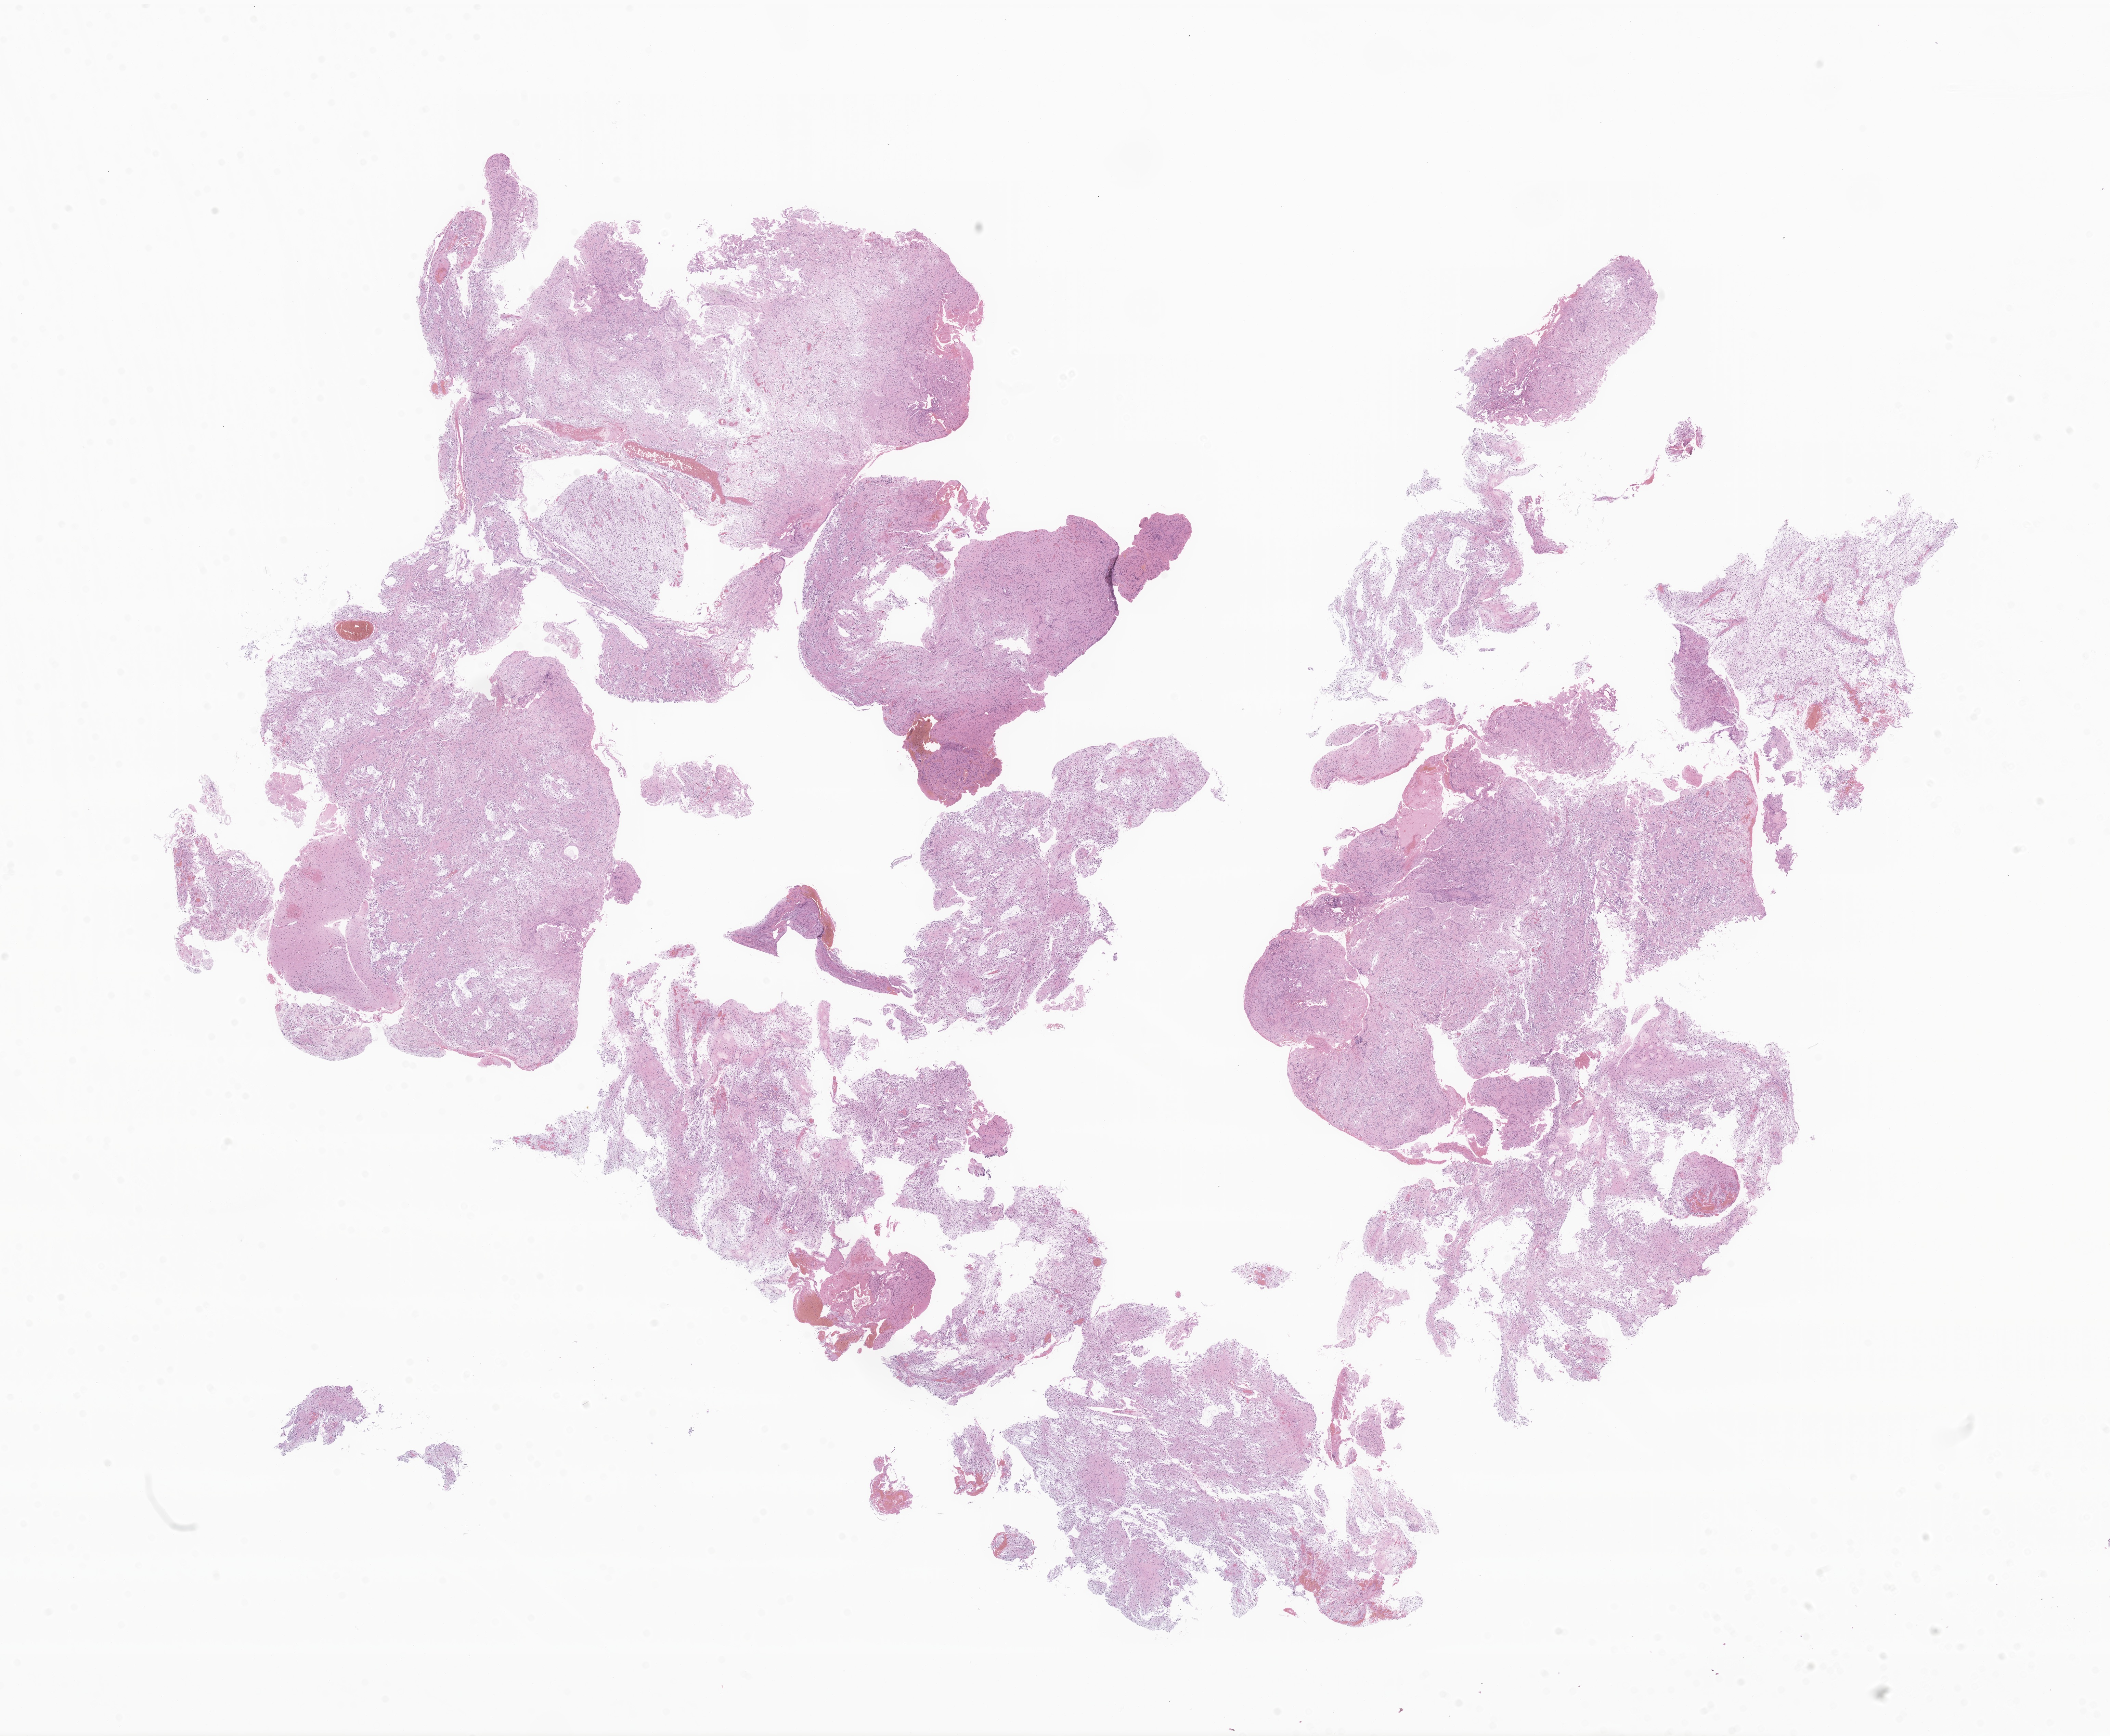
Whole-slide image, haematoxylin and eosin stain of tumor tissue from the brain — whole scanned area (about 26.0 x 21.4 mm) shown as a low-resolution overview, formalin-fixed, paraffin-embedded (FFPE) tissue. Patient male; age 37 months (3 years 1 month).
Recorded diagnosis: Pilocytic astrocytoma.